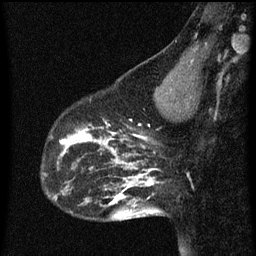
Breast MRI (dynamic contrast-enhanced), one sagittal slice; slice 19 of 60 in the series (ordered by position); dynamic contrast-enhanced series, image 2 of 3 at this slice position (ordered by acquisition); 1.5 T; TE 4.2 ms, TR 8 ms; 2 mm slice thickness; 256 × 256 image matrix, field of view 180 × 180 mm. Patient: female, 43 years.
Structures marked on this image (semi-automatic segmentation, software-assisted and operator-edited):
- analysis volume of interest (the breast-tissue region the enhancement analysis was run in; not a lesion): bounding box <53,104,101,155> (left, top, right, bottom; pixels)
- tumour enhancement mask (voxels above the 70 % enhancement threshold inside the analysis volume of interest): <61,126,101,155>